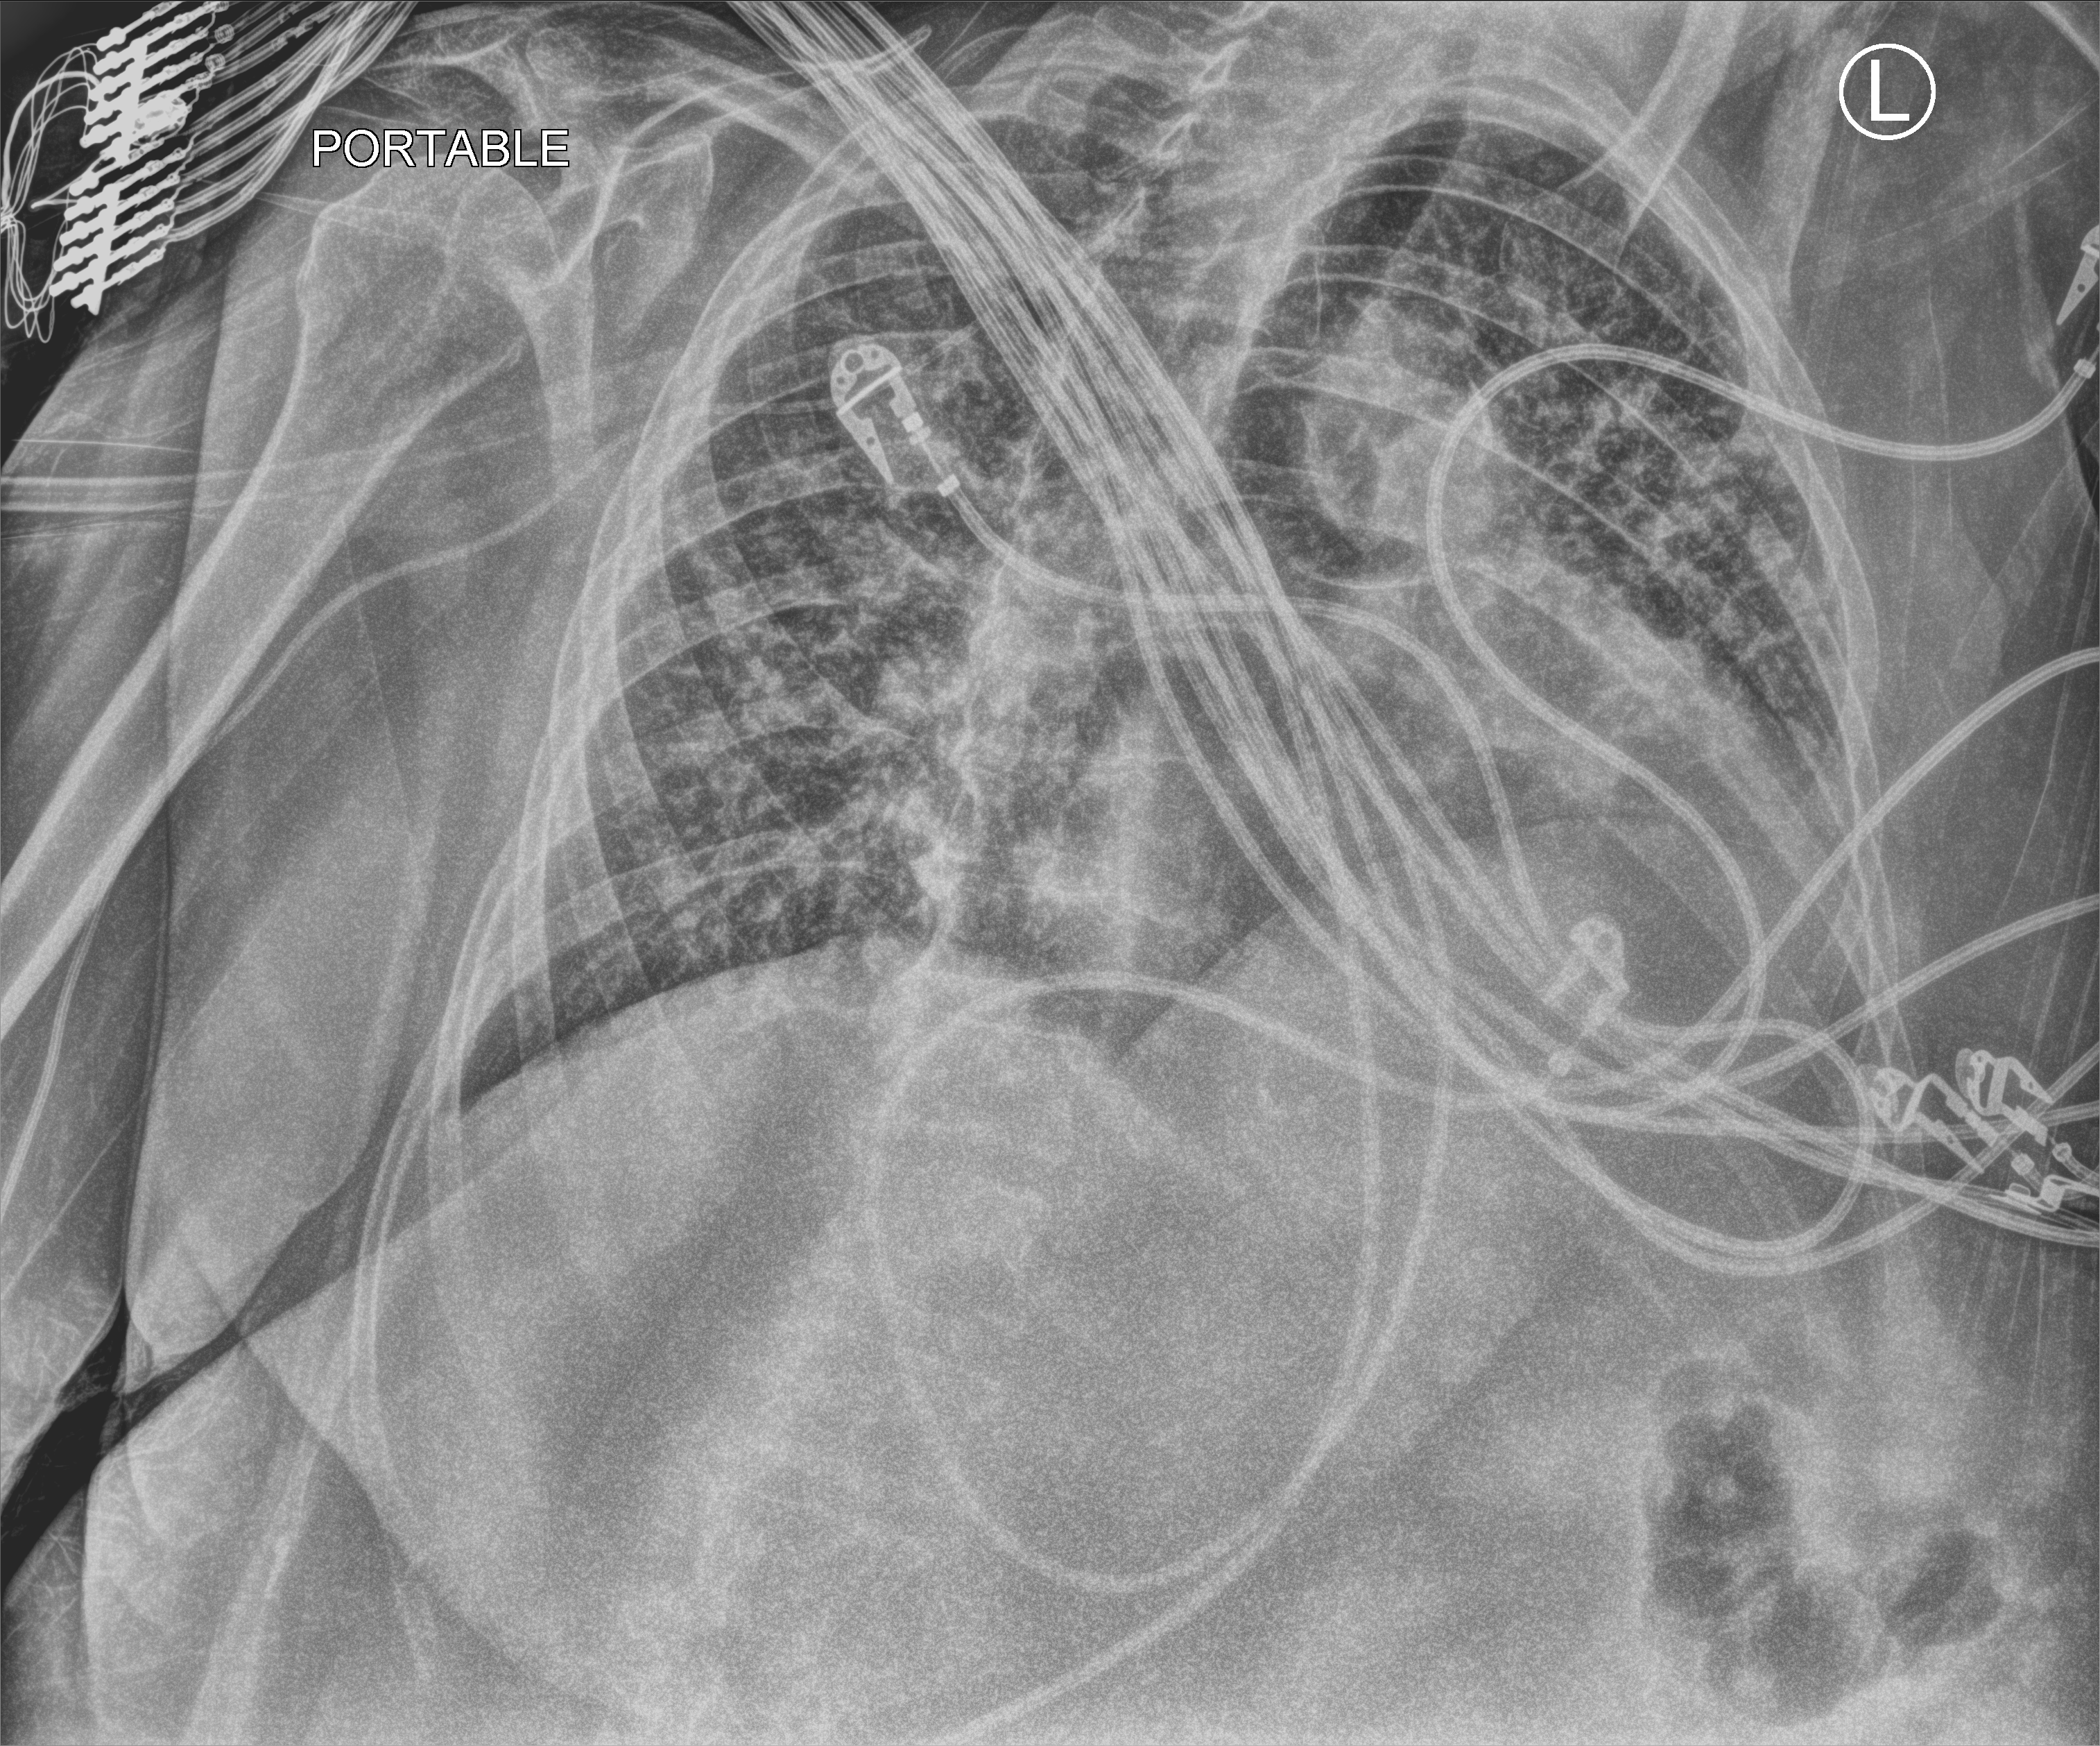
Portable chest radiograph, anteroposterior (AP) projection. Patient hospitalised with COVID-19; female, aged 75–90 years.
Hospital-stay facts (about this admission, not read from this image; timing relative to this image not recorded):
- mechanically ventilated during this hospital stay: yes
- admitted to intensive care during this hospital stay: yes
- diabetes (admission record): no